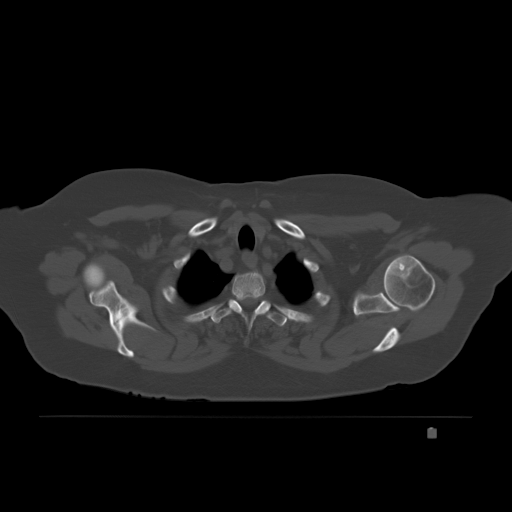
CT including the spine, one axial slice. Slice 170 of 221 in the series (ordered by position). Bone window (W 1800 / L 400 HU). 512 × 512 image matrix, field of view 474 × 474 mm. Female patient, age 63 years. Case-level facts recorded for this patient, not image findings: primary cancer: breast.
Structures marked on this image (semi-automatic segmentation, software-assisted and operator-edited):
- T3 vertebra: bounding box (x1, y1, x2, y2) in pixels: (266, 315, 285, 320)